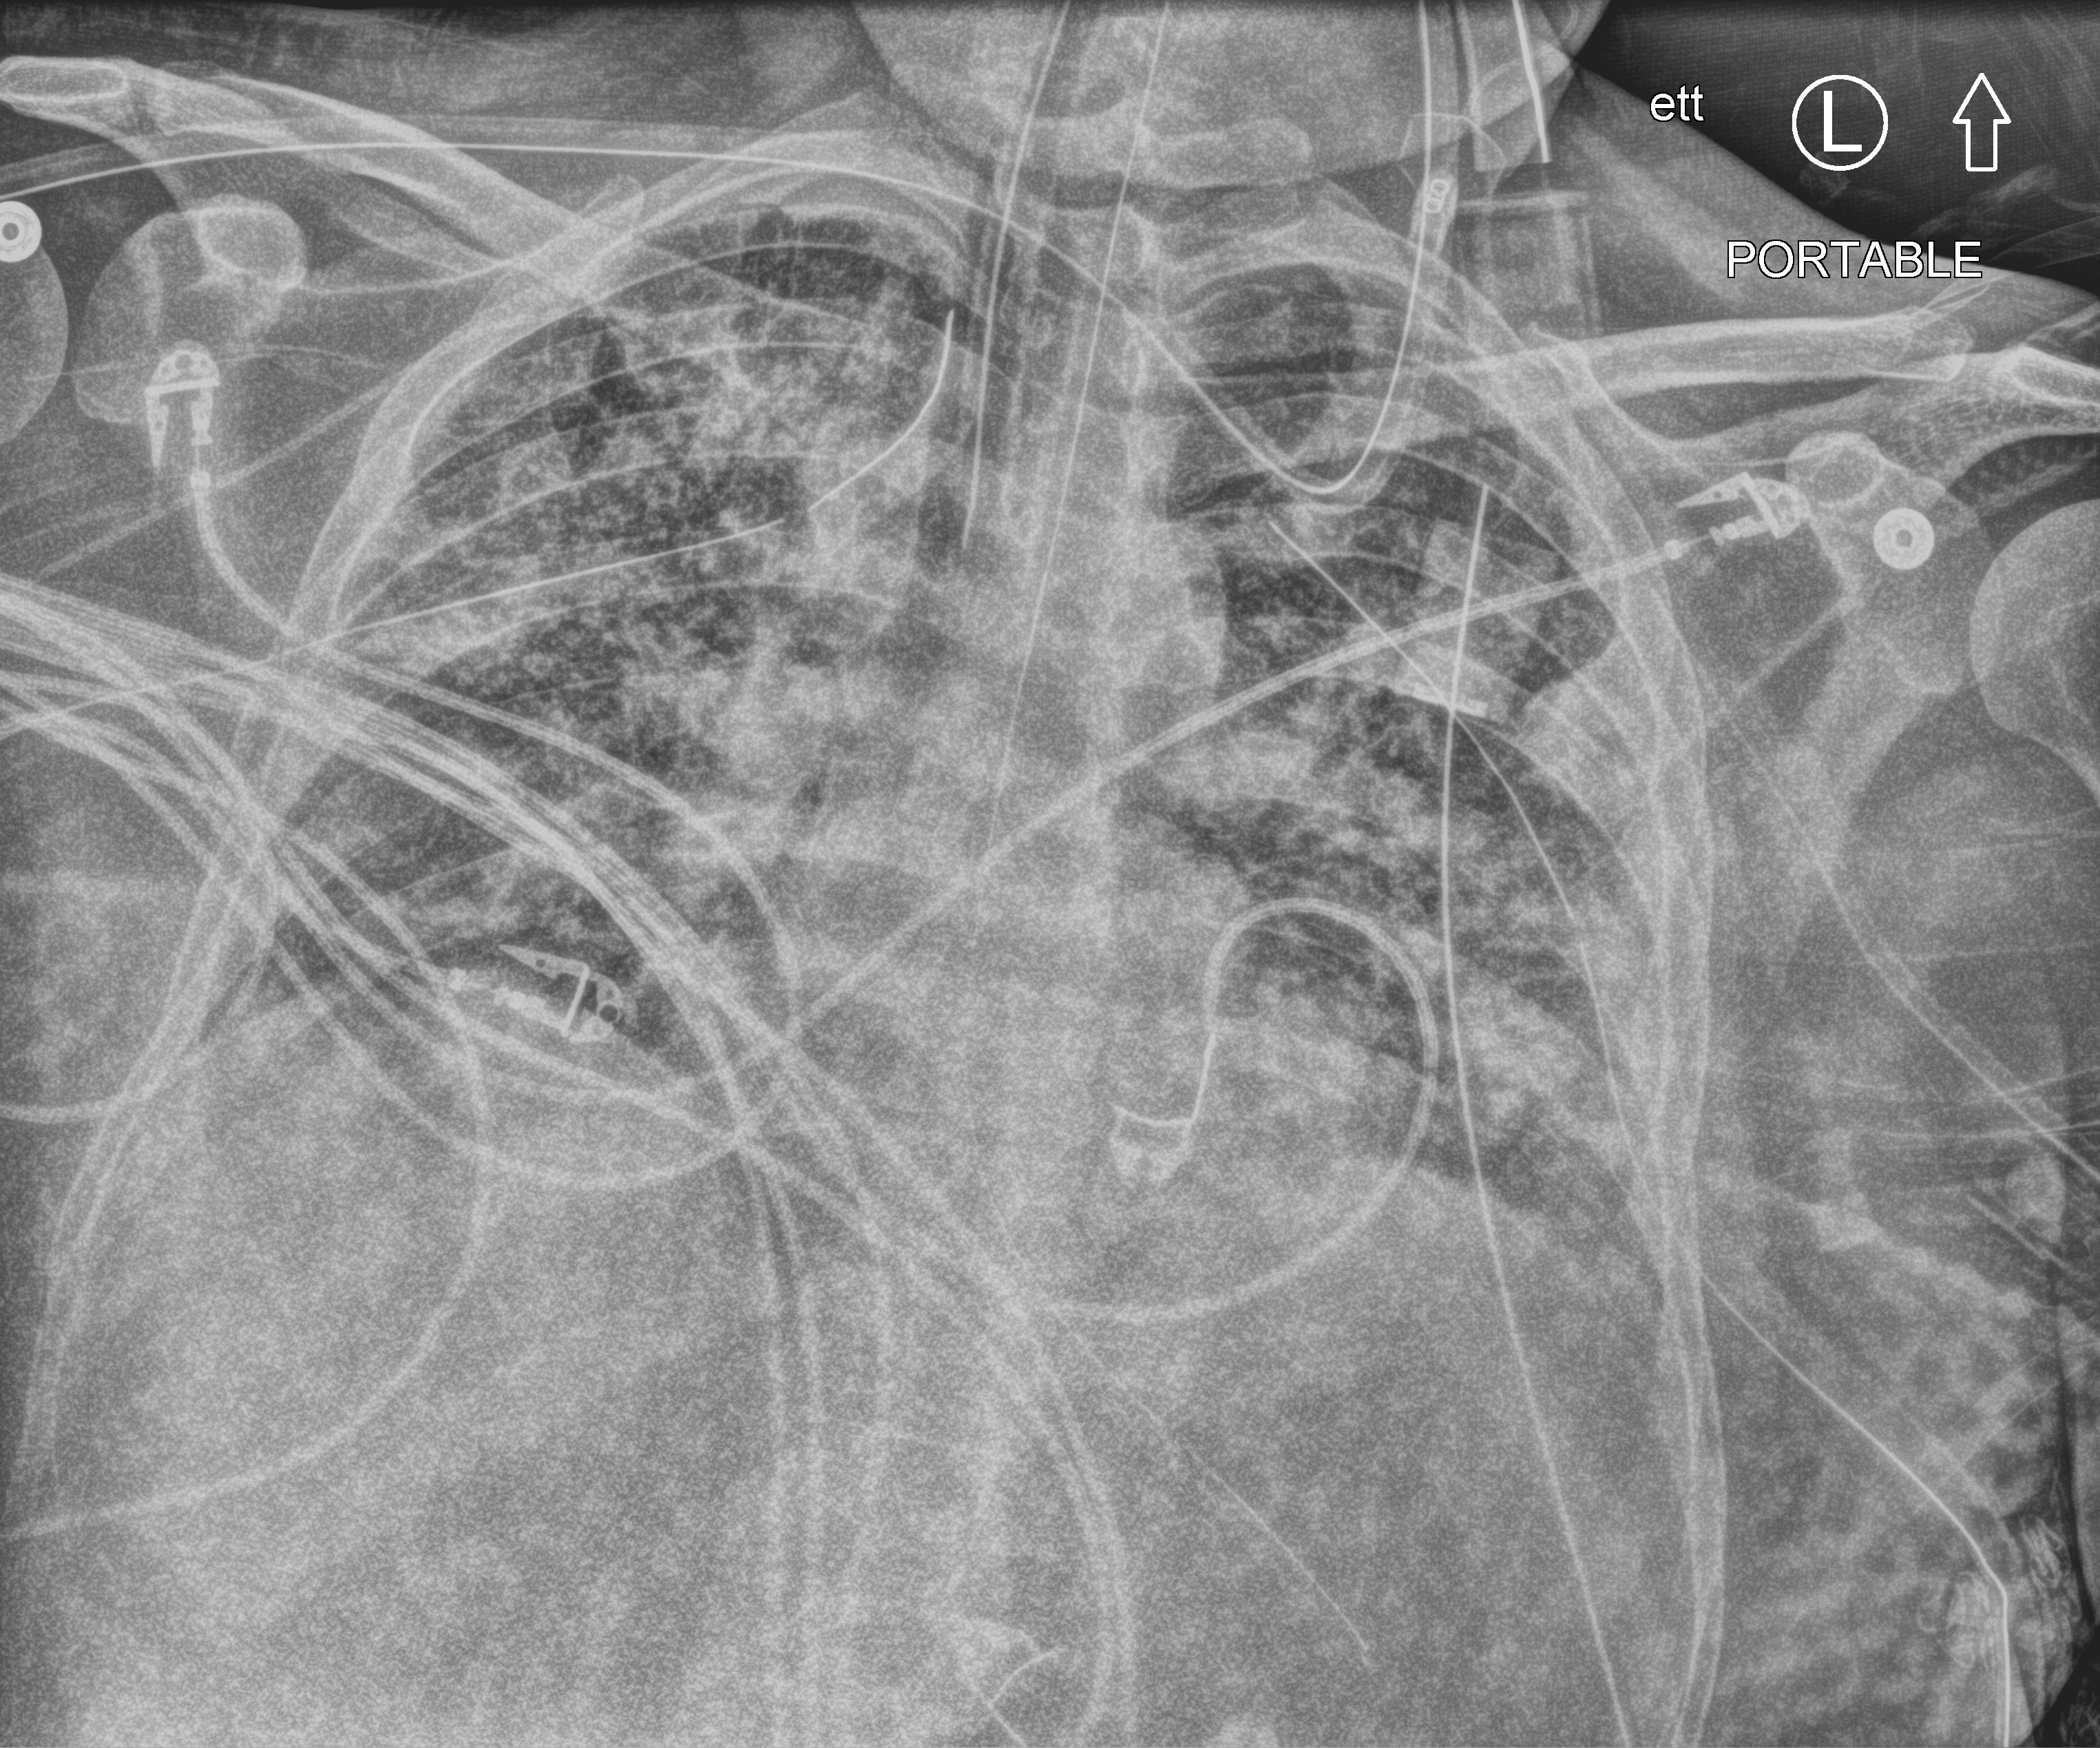
Portable chest radiograph. Patient hospitalised with COVID-19; male, aged 18–59 years.
Hospital-stay facts (about this admission, not read from this image; timing relative to this image not recorded):
- length of hospital stay: 63 days